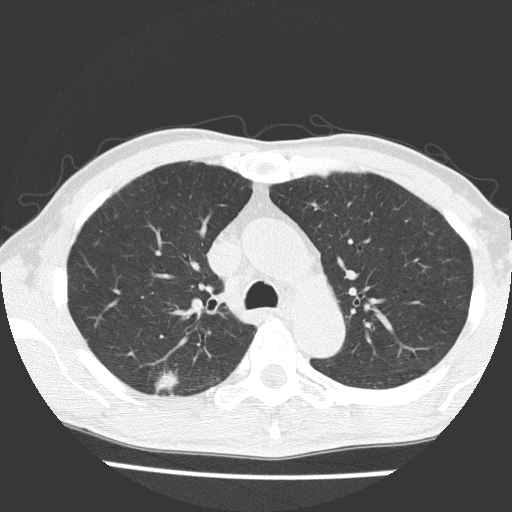
Low-dose screening chest CT, one axial slice. Slice 113 of 160 in the series (ordered by position). 120 kVp. Lung window (W 1500 / L -600 HU). 2 mm slice thickness. 512 × 512 image matrix, field of view 309 × 309 mm.
Structures marked on this image (manually delineated by an expert):
- lesion 1 (tumor, upper lobe of right lung): bounding box (x1, y1, x2, y2) in pixels: (155, 371, 179, 393)